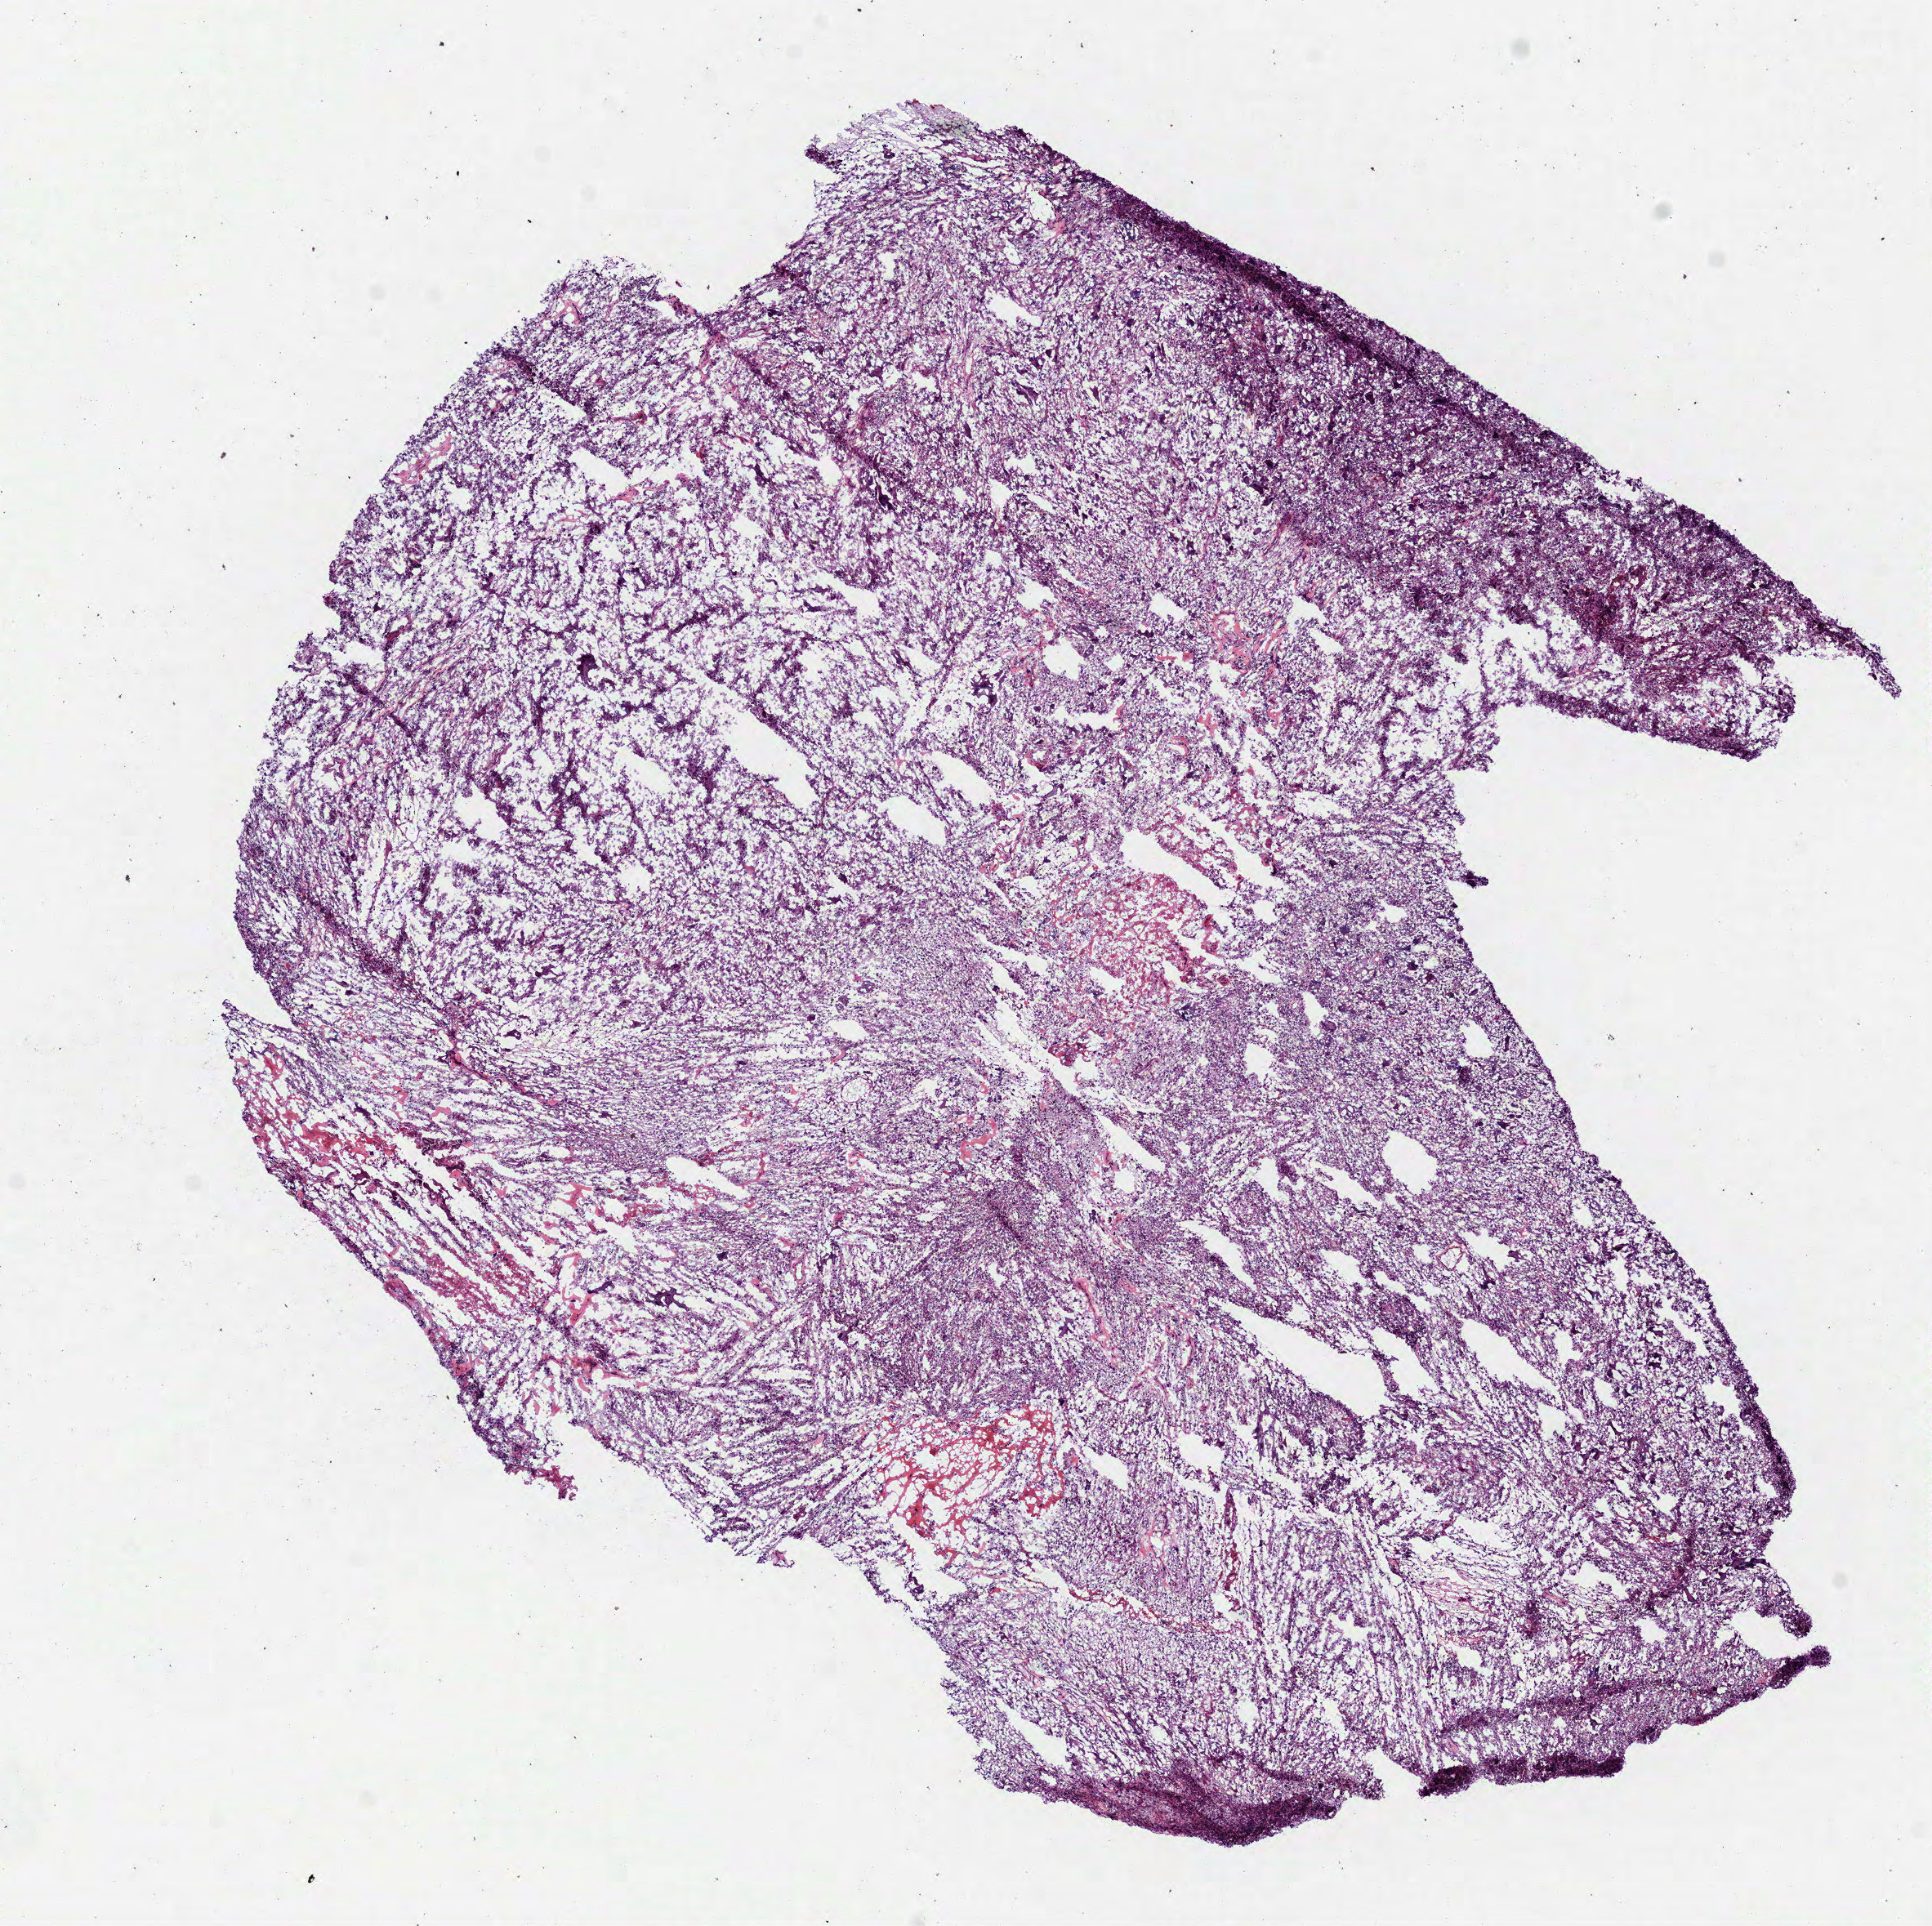
Whole-slide histology image, H&E — whole scanned area (about 9.5 x 9.5 mm) shown as a low-resolution overview. Frozen section from the bottom of the tissue portion. Brain, primary tumour sample. Female, age 53 years at initial diagnosis. Pathologist review of this section (percent, as recorded): tumour cells 90%, tumour nuclei 85%, normal cells 0%, stromal cells 0%, necrosis 10%.
Pathologic diagnosis: Glioblastoma.